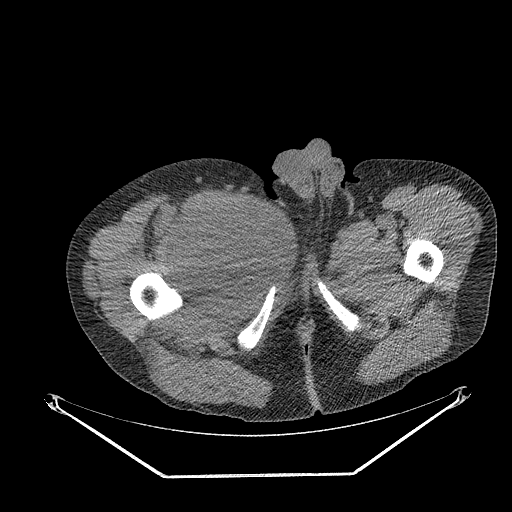
CT of an extremity soft-tissue mass (from a PET/CT study), one axial slice; position 283 of 311 along the scan axis; 140 kVp; soft-tissue window (W 400 / L 40 HU); 512 × 512 image matrix. Male patient. Case-level facts recorded for this patient, not image findings: histological type: undifferentiated - pleiomorphic; grade: high; site of the primary tumour: right thigh.
Structures marked on this image (expert contour drawn on MRI and transferred to this co-registered scan by the dataset authors):
- gross tumour volume including surrounding oedema: box from (x=185, y=196) to (x=259, y=275) px
- gross tumour volume (mass): (x=183, y=201)–(x=257, y=273)